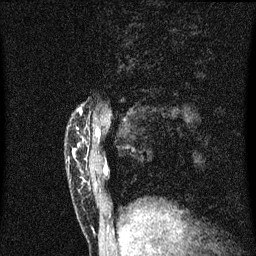
Breast MRI (dynamic contrast-enhanced), one sagittal slice; slice 11 of 60 in the series (ordered by position); dynamic contrast-enhanced series, image 2 of 3 at this slice position (ordered by acquisition); 1.5 T; TE 4.2 ms, TR 8.4 ms; 2 mm slice thickness; 256 × 256 image matrix, field of view 200 × 200 mm. Patient: female, 40 years.
Annotated regions visible in this slice (semi-automatic segmentation, software-assisted and operator-edited):
- analysis volume of interest (the breast-tissue region the enhancement analysis was run in; not a lesion): box from (x=74, y=108) to (x=102, y=203) px
- tumour enhancement mask (voxels above the 70 % enhancement threshold inside the analysis volume of interest): (x=80, y=108)–(x=83, y=115)